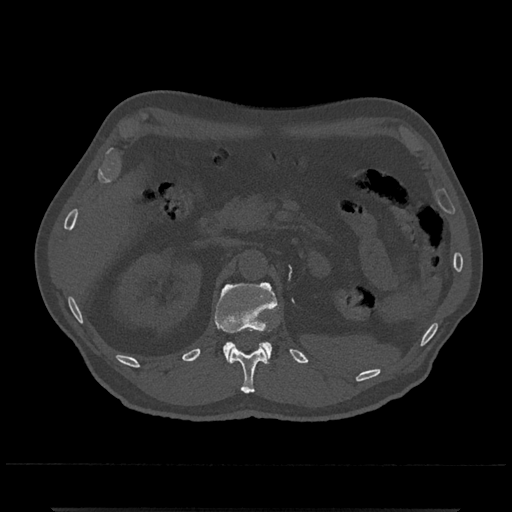
CT including the spine, one axial slice; position 397 of 797 along the scan axis; bone window (W 1800 / L 400 HU); 0.5 mm slice thickness; 512 × 512 image matrix, field of view 393 × 393 mm. Patient: male, 67 years. From the clinical record (not read from this slice): primary cancer: prostate.
Annotated regions visible in this slice (semi-automatic segmentation, software-assisted and operator-edited):
- L1 vertebra: box from (x=214, y=282) to (x=278, y=363) px
- T12 vertebra: (x=230, y=330)–(x=268, y=394)